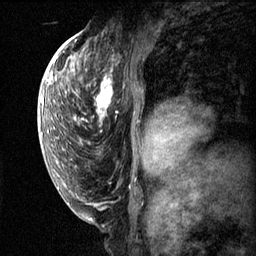
Breast MRI (dynamic contrast-enhanced), one sagittal slice; slice 36 of 60 in the series (ordered by position); dynamic contrast-enhanced series, image 2 of 3 at this slice position (ordered by acquisition); 1.5 T; TE 4.2 ms, TR 11.1 ms; 256 × 256 image matrix, field of view 180 × 180 mm. Patient: female, 50 years.
Structures marked on this image (semi-automatically segmented with operator editing):
- analysis volume of interest (the breast-tissue region the enhancement analysis was run in; not a lesion): bounding box (x1, y1, x2, y2) in pixels: (82, 56, 168, 143)
- tumour enhancement mask (voxels above the 70 % enhancement threshold inside the analysis volume of interest): (82, 58, 160, 143)